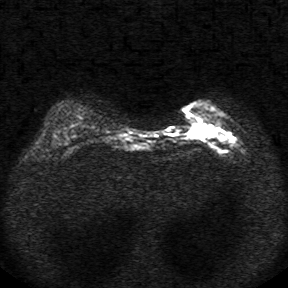
Breast MRI, one axial slice. Position 10 of 34 along the scan axis. Diffusion-weighted series; image 2 of 4 stored at this slice position (different b-values; order by instance number). 1.5 T. 288 × 288 image matrix. Female patient.
Structures marked on this image (manually delineated by an expert):
- tumour on diffusion-weighted imaging: bounding box (x1, y1, x2, y2) in pixels: (189, 124, 216, 138)